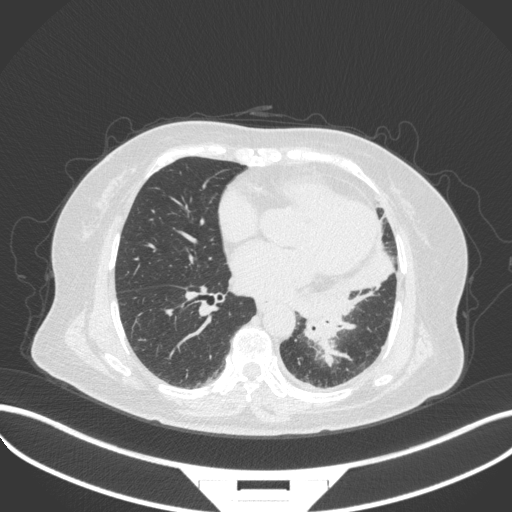
Chest CT, one axial slice; position 152 of 328 along the scan axis; reconstruction kernel B31f; 120 kVp; lung window (W 1500 / L -600 HU); 1 mm slice thickness; 512 × 512 image matrix, field of view 400 × 400 mm. Patient: female, 69 years. Case-level facts recorded for this patient, not image findings: clinical TNM (as recorded): T2b N3 M1.
Outlined on this slice (rectangle marked by the reading radiologist):
- lung tumour (recorded histology: adenocarcinoma): bounding box <298,301,355,366> (left, top, right, bottom; pixels)